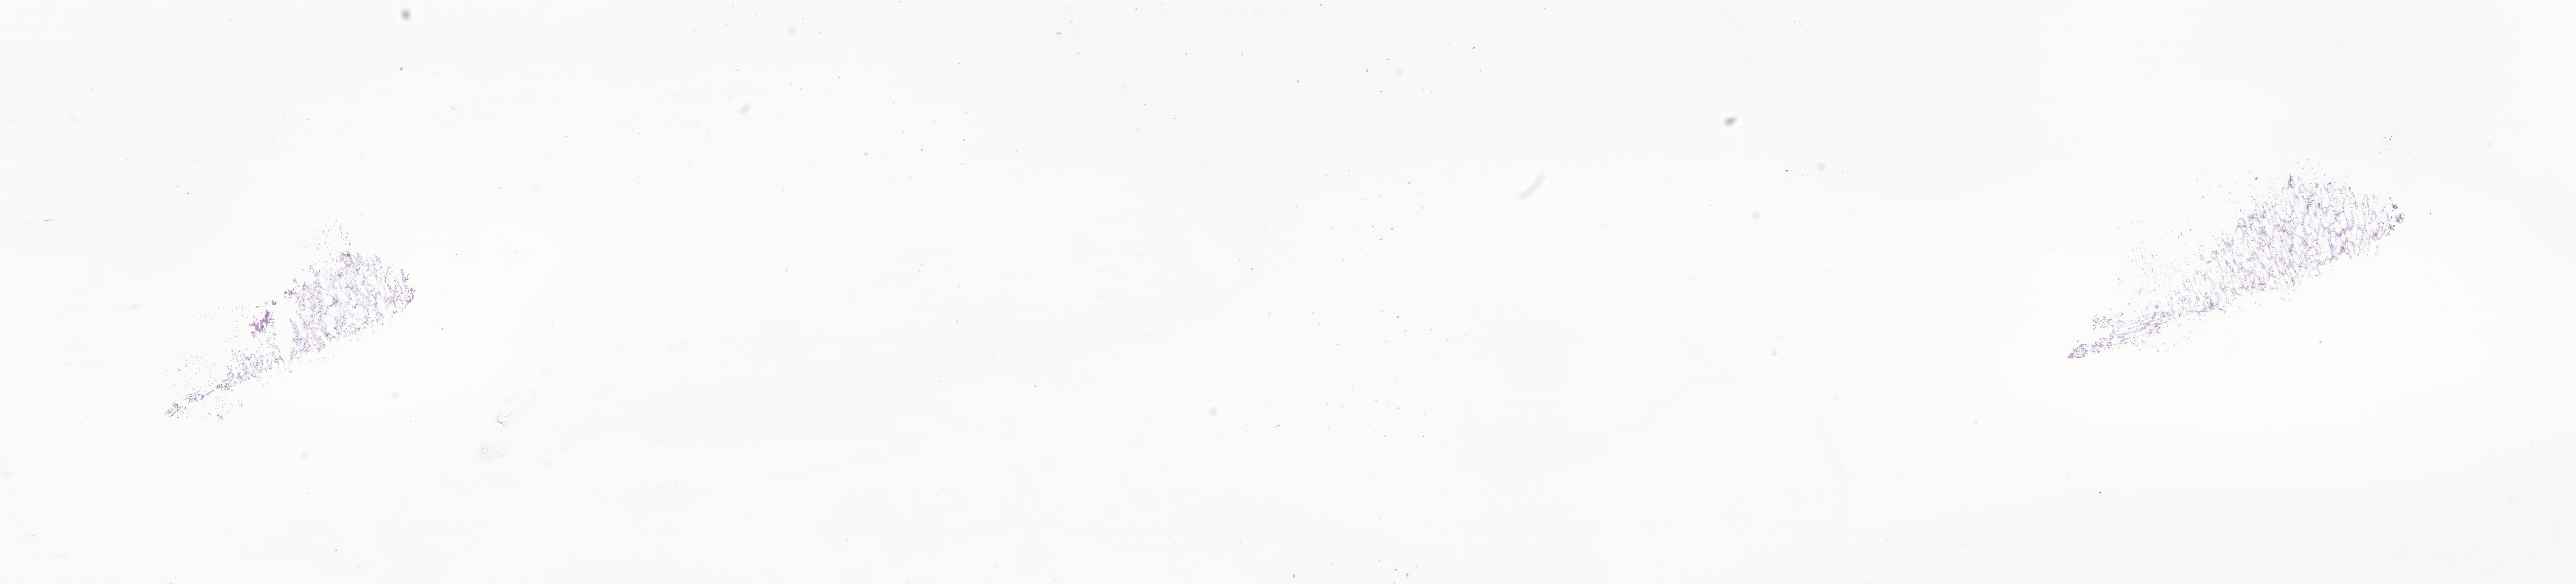
Whole-slide image, hematoxylin and eosin (H&E) stain of tumor tissue from the brain, a low-resolution overview of the entire scanned area, about 29.4 x 6.7 mm. Frozen section. Patient male; age 38 months (3 years 2 months).
Diagnosis: Pilocytic astrocytoma.